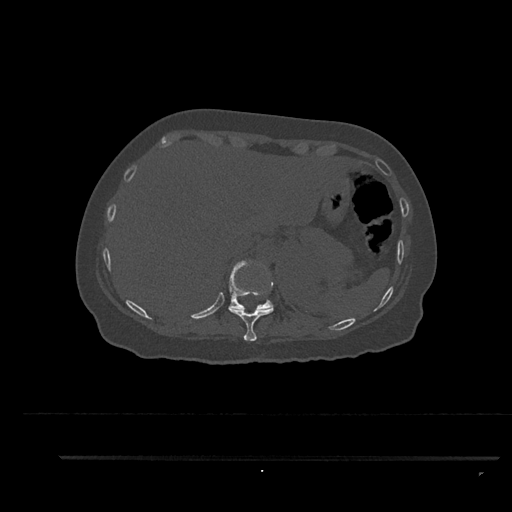
CT including the spine, one axial slice. Slice 343 of 797 in the series (ordered by position). Reconstruction kernel Br40s/3. 120 kVp. Bone window (W 1800 / L 400 HU). 0.5 mm slice thickness. 512 × 512 image matrix. Female patient, age 44 years. From the clinical record (not read from this slice): primary cancer: renal; vertebrae with lytic lesions (as recorded): L1.
Outlined on this slice (semi-automatic segmentation, software-assisted and operator-edited):
- T10 vertebra: bounding box (x1, y1, x2, y2) in pixels: (228, 306, 274, 341)
- T11 vertebra: (229, 259, 274, 310)